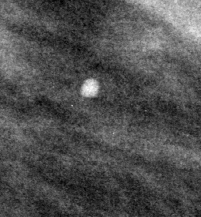
Crop from a digitized film mammogram around one marked abnormality, left breast, MLO view.
Marked abnormality: calcifications, morphology punctate; BI-RADS assessment category 2; benign without callback (not worked up further).